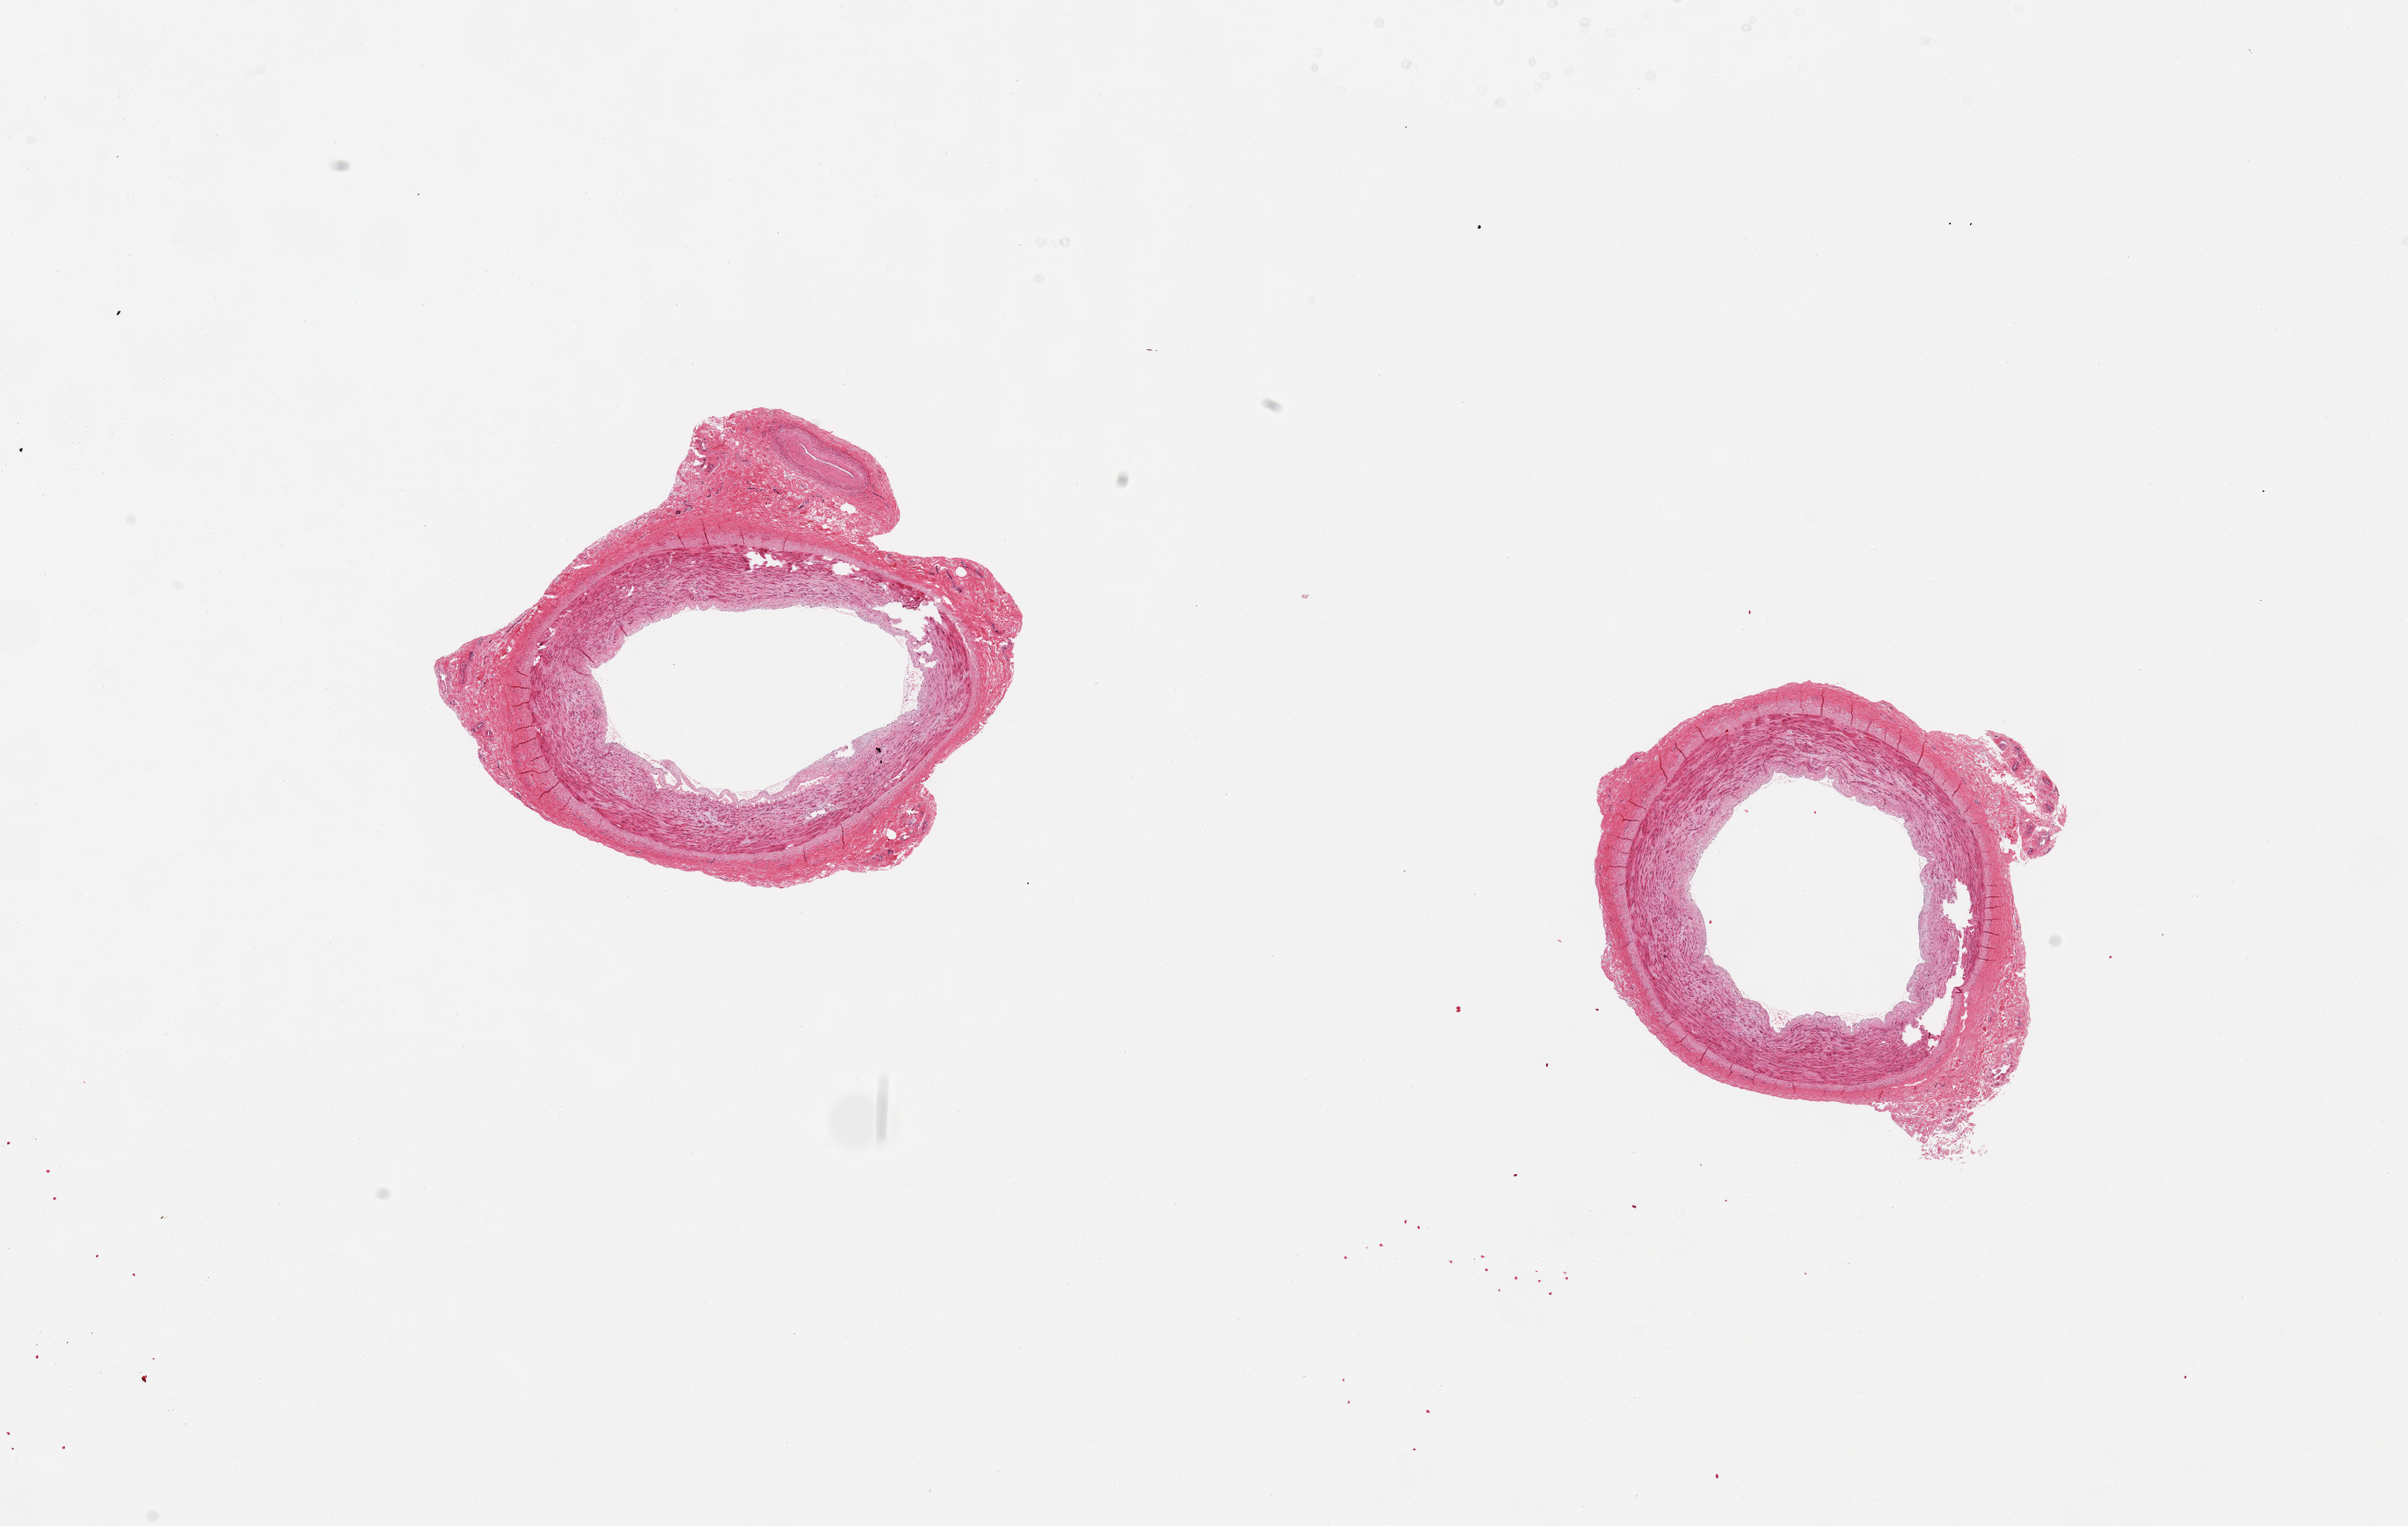
Whole-slide image, haematoxylin and eosin stain, brightfield, whole scanned area (about 21.7 x 13.7 mm, from a 20x scan) shown as a low-resolution overview, PAXgene-fixed, paraffin-embedded tissue, section of tibial artery (target tissue), tissue donor sample. Female donor.
* pathologist's review note for this sample: 2 aliquots, ~4mm d. Good clean specimens